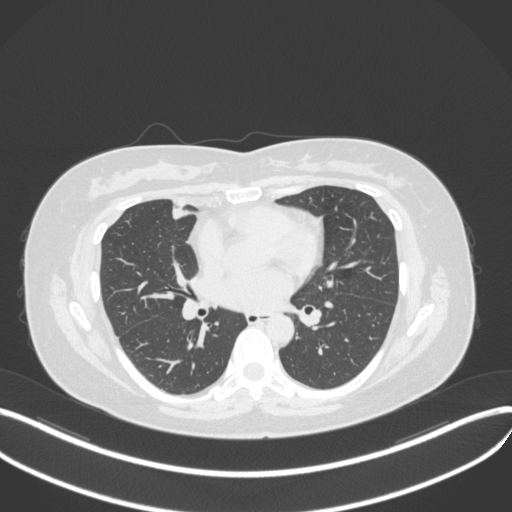
Chest CT, one axial slice; slice 154 of 272 in the series (ordered by position); 120 kVp; lung window (W 1500 / L -600 HU); 512 × 512 image matrix. Female patient, age 42 years. Case-level facts recorded for this patient, not image findings: clinical TNM (as recorded): T1b N0 M0.
Structures marked on this image (rectangle marked by the reading radiologist):
- lung tumour (recorded histology: adenocarcinoma): bounding box <168,202,198,227> (left, top, right, bottom; pixels)